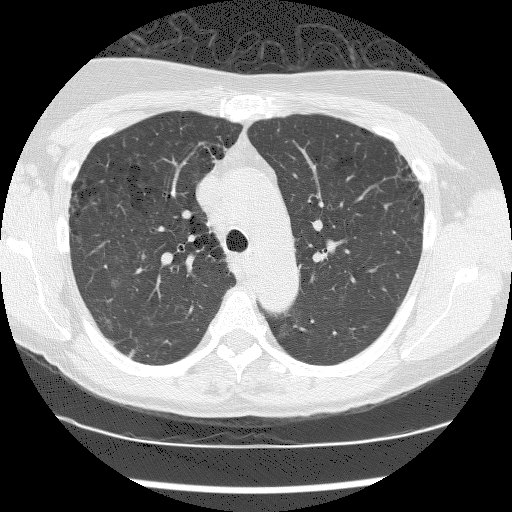
Low-dose screening chest CT, one axial slice. Slice 129 of 176 in the series (ordered by position). Lung window (W 1500 / L -600 HU). 2.5 mm slice thickness. 512 × 512 image matrix, field of view 320 × 320 mm.
Outlined on this slice (outlined manually by an expert reader):
- lesion 1 (tumor, lower lobe of right lung): bounding box <130,349,135,357> (left, top, right, bottom; pixels)